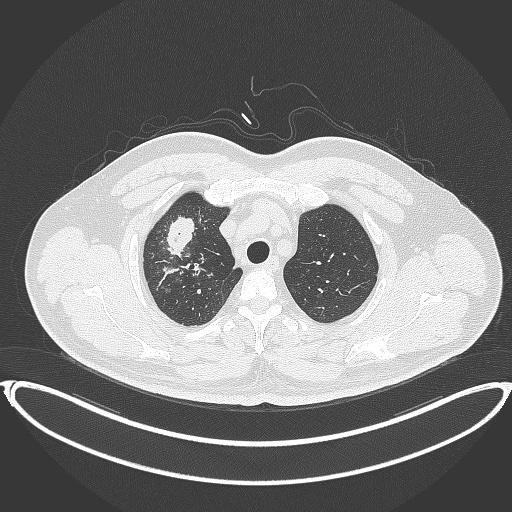
Chest CT, one axial slice. Position 322 of 399 along the scan axis. Reconstruction kernel B70f. 120 kVp. Lung window (W 1500 / L -600 HU). 1 mm slice thickness. 512 × 512 image matrix, field of view 445 × 445 mm. Patient: male, 53 years. From the clinical record (not read from this slice): clinical TNM (as recorded): T2a N0 M0.
Outlined on this slice (rectangle marked by the reading radiologist):
- lung tumour (recorded histology: adenocarcinoma): box from (x=165, y=214) to (x=200, y=262) px